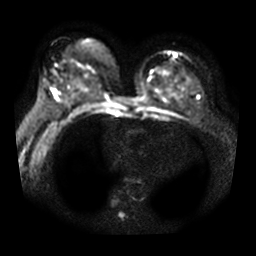
Breast MRI, one axial slice. Position 18 of 36 along the scan axis. Diffusion-weighted series; image 2 of 4 stored at this slice position (different b-values; order by instance number). 3 T. 256 × 256 image matrix, field of view 340 × 340 mm. Female patient.
Structures marked on this image (manually delineated by an expert):
- tumour on diffusion-weighted imaging: bounding box <53,90,56,93> (left, top, right, bottom; pixels)